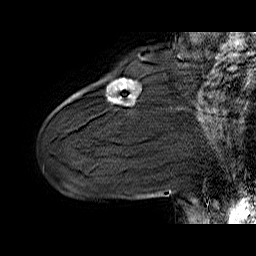
Breast MRI (dynamic contrast-enhanced), one sagittal slice; position 15 of 60 along the scan axis; dynamic contrast-enhanced series, time point 2 of 6 at this slice position (early post-contrast); 1.5 T; TE 6.4 ms, TR 32.9 ms; 4 mm slice thickness; 256 × 256 image matrix, field of view 200 × 200 mm. Female patient. Case-level facts recorded for this patient, not image findings: setting: breast cancer imaged before/during neoadjuvant chemotherapy; receptor status: HER2-positive.
Outlined on this slice (semi-automatically segmented with operator editing):
- analysis volume of interest (the breast-tissue region the enhancement analysis was run in; not a lesion): bounding box <102,79,141,106> (left, top, right, bottom; pixels)
- tumour enhancement mask (voxels above the 100 % enhancement threshold inside the analysis volume of interest): <109,79,132,102>